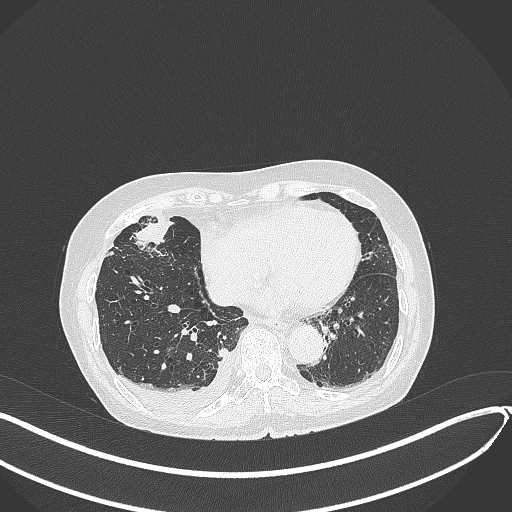
Chest CT, one axial slice; position 126 of 418 along the scan axis; reconstruction kernel B70f; lung window (W 1500 / L -600 HU); 1 mm slice thickness; 512 × 512 image matrix, field of view 400 × 400 mm. Patient: female, 75 years. Case-level facts recorded for this patient, not image findings: clinical TNM (as recorded): T2a N3 M0.
Annotated regions visible in this slice (rectangle marked by the reading radiologist):
- lung tumour (recorded histology: adenocarcinoma): bounding box <131,218,171,250> (left, top, right, bottom; pixels)